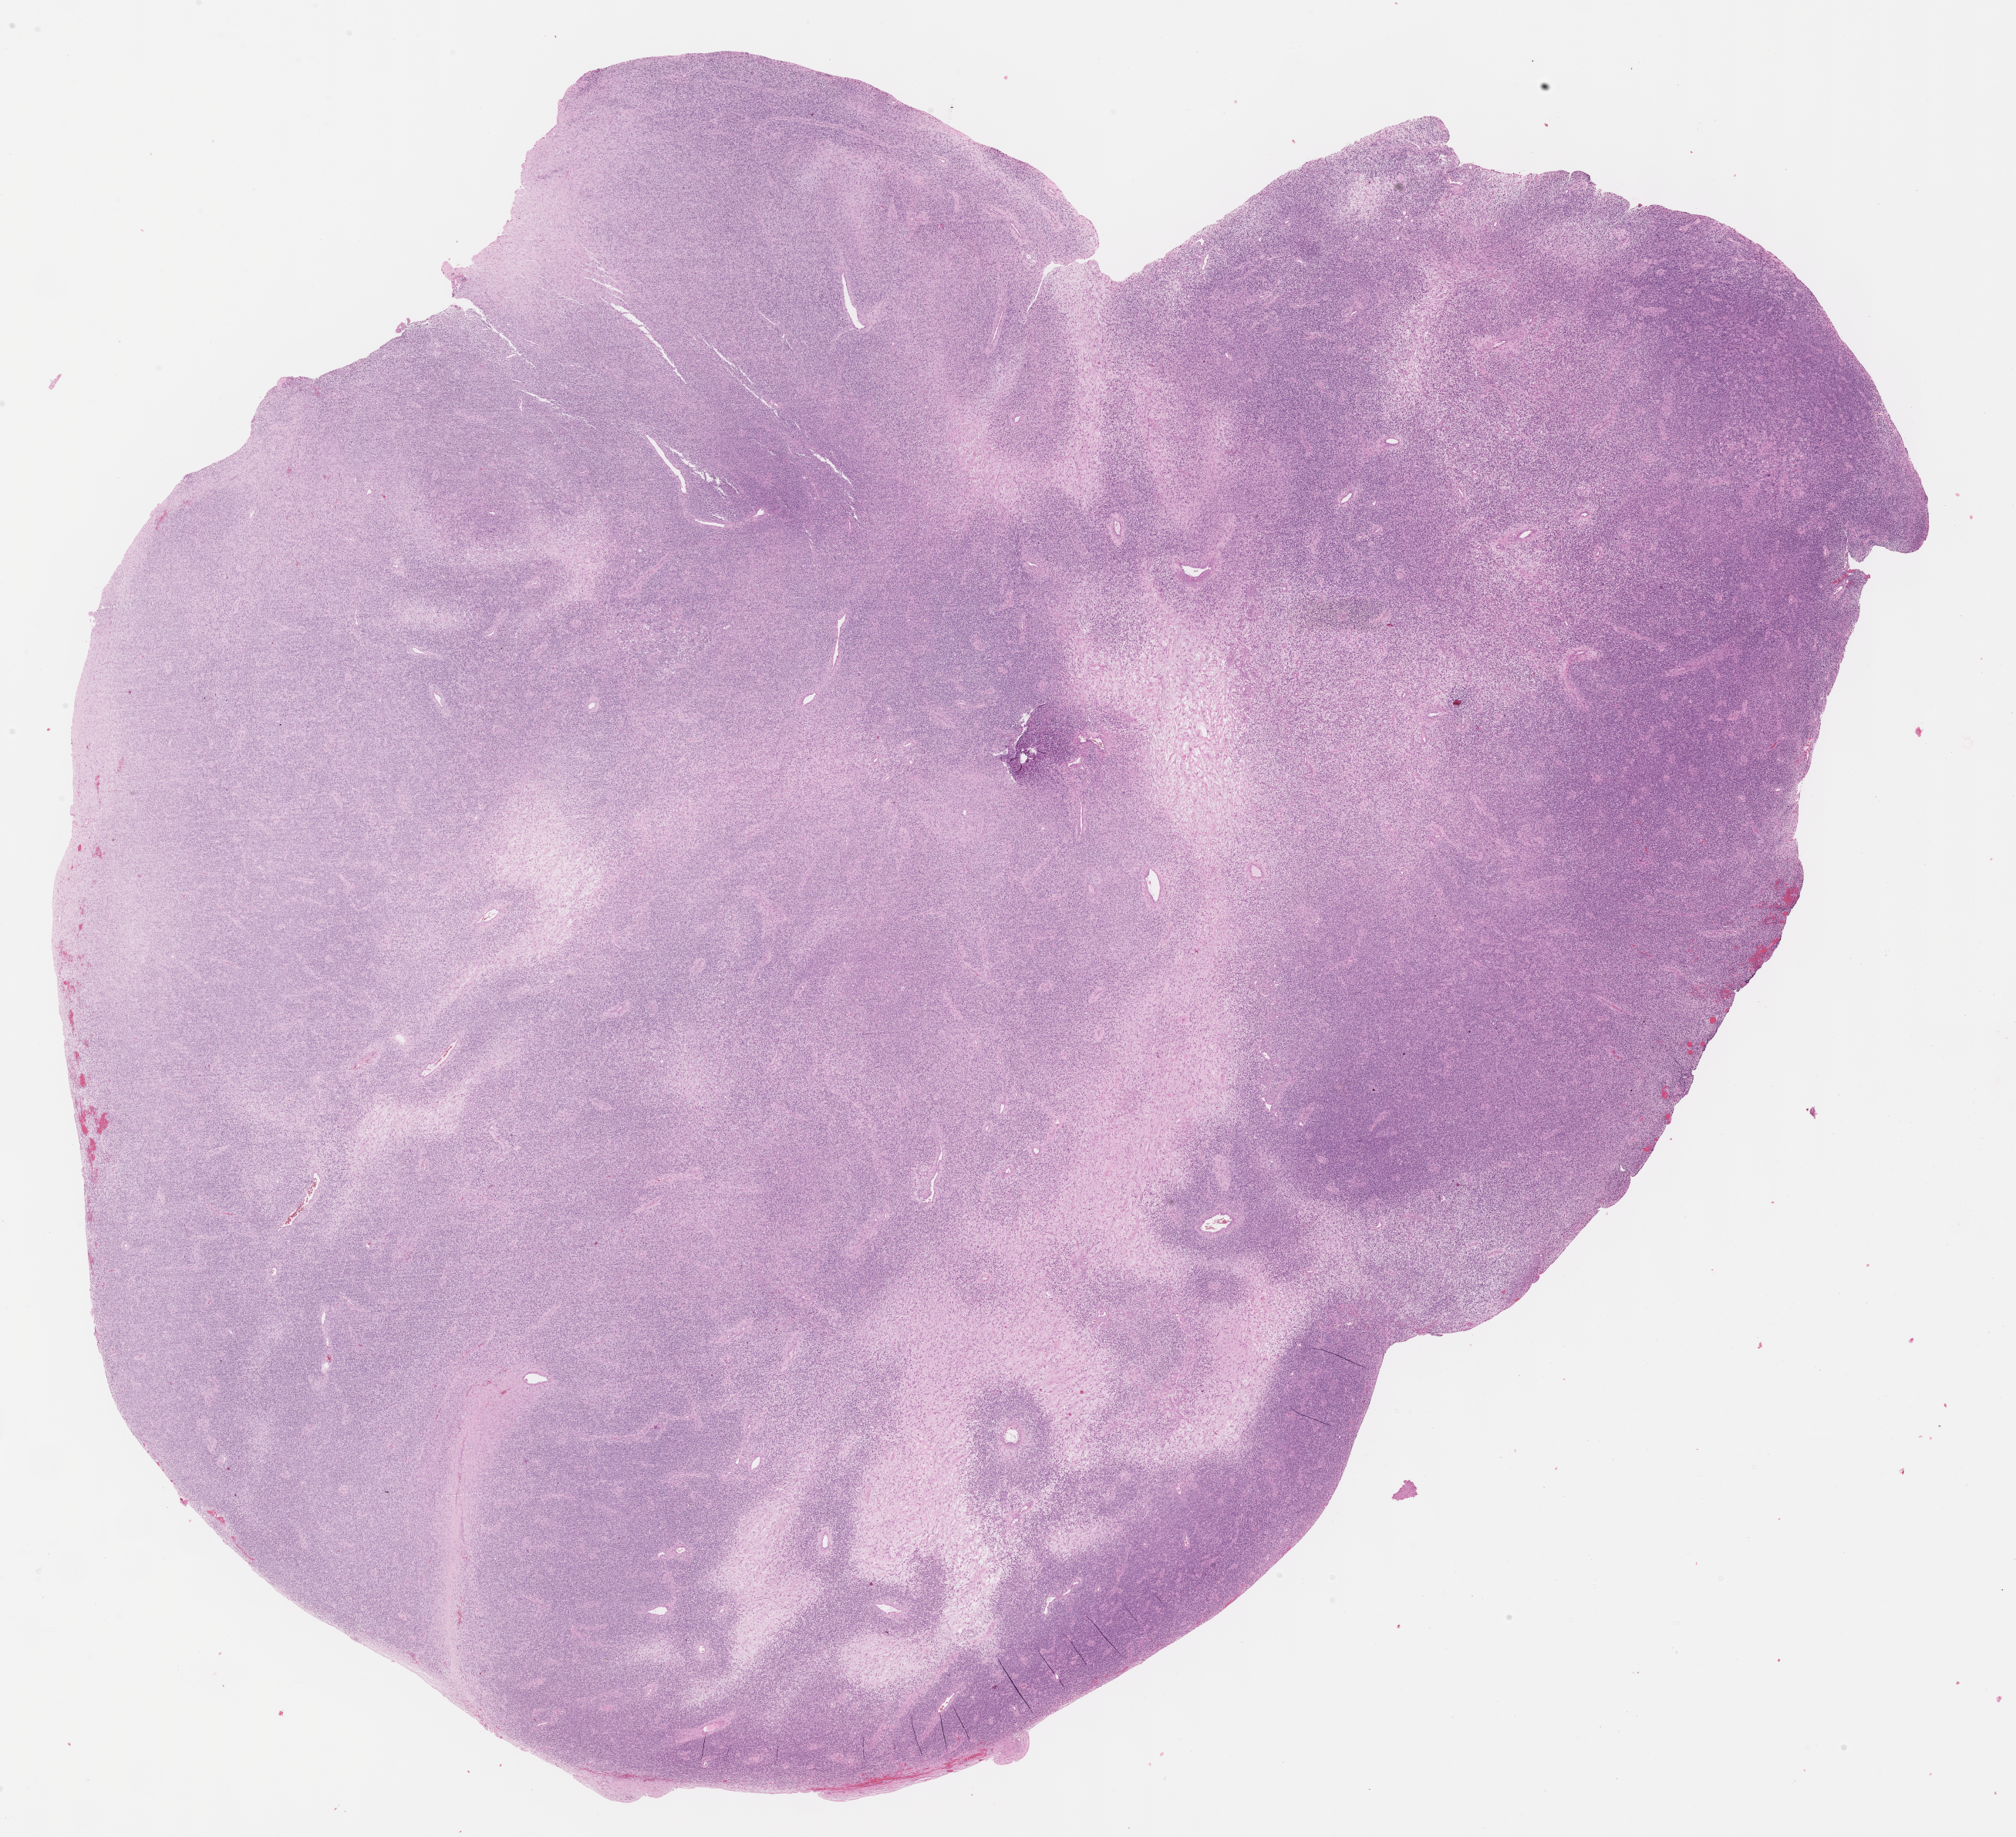
H&E whole-slide image of tumor tissue, shown as a low-resolution overview of the whole scanned area (about 21.1 x 19.3 mm). Formalin-fixed, paraffin-embedded (FFPE) tissue. Patient: female, age 1.1 years at diagnosis.
* stage (as recorded): 1
* diagnosis: rhabdomyosarcoma; histological classification: embryonal rhabdomyosarcoma
* metastatic status at presentation (as recorded): non-metastatic